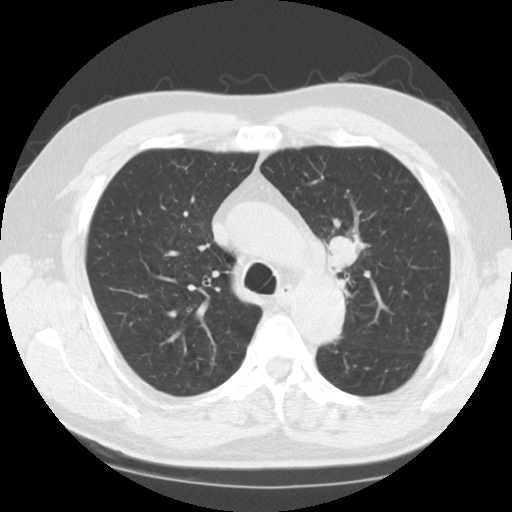
Low-dose screening chest CT, one axial slice; slice 90 of 124 in the series (ordered by position); reconstruction kernel STANDARD; 120 kVp; lung window (W 1500 / L -600 HU); 2.5 mm slice thickness; 512 × 512 image matrix, field of view 340 × 340 mm.
Structures marked on this image (manually delineated by an expert):
- lesion 1 (tumor, upper lobe of left lung): box from (x=327, y=235) to (x=358, y=271) px